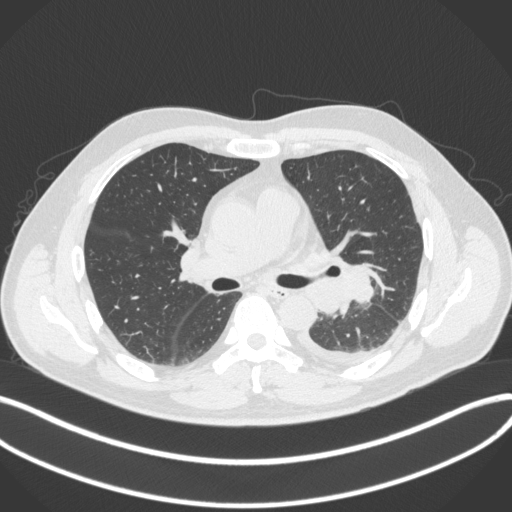
Chest CT, one axial slice; slice 212 of 350 in the series (ordered by position); reconstruction kernel B31f; lung window (W 1500 / L -600 HU); 1 mm slice thickness; 512 × 512 image matrix. Patient: male, 58 years. Case-level facts recorded for this patient, not image findings: clinical TNM (as recorded): T3 N1 M1b.
Structures marked on this image (bounding box drawn by a radiologist):
- lung tumour (recorded histology: small cell carcinoma): bounding box [x1, y1, x2, y2] px = [314, 261, 376, 312]